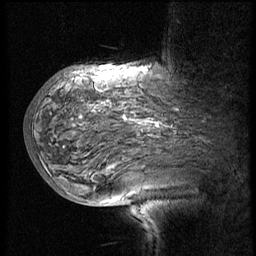
Breast MRI (dynamic contrast-enhanced), one sagittal slice; slice 41 of 60 in the series (ordered by position); 3 images stored at this slice position (order not interpretable as contrast timing); 1.5 T; TE 4.2 ms, TR 8.9 ms; 2.5 mm slice thickness; 256 × 256 image matrix, field of view 200 × 200 mm. Patient: female, 57 years. Case-level facts recorded for this patient, not image findings: setting: breast cancer imaged before/during neoadjuvant chemotherapy; receptor status: HER2-positive.
Structures marked on this image (semi-automatic segmentation, software-assisted and operator-edited):
- analysis volume of interest (the breast-tissue region the enhancement analysis was run in; not a lesion): bounding box [x1, y1, x2, y2] px = [34, 75, 214, 171]
- tumour enhancement mask (voxels above the 140 % enhancement threshold inside the analysis volume of interest): [147, 120, 161, 127]